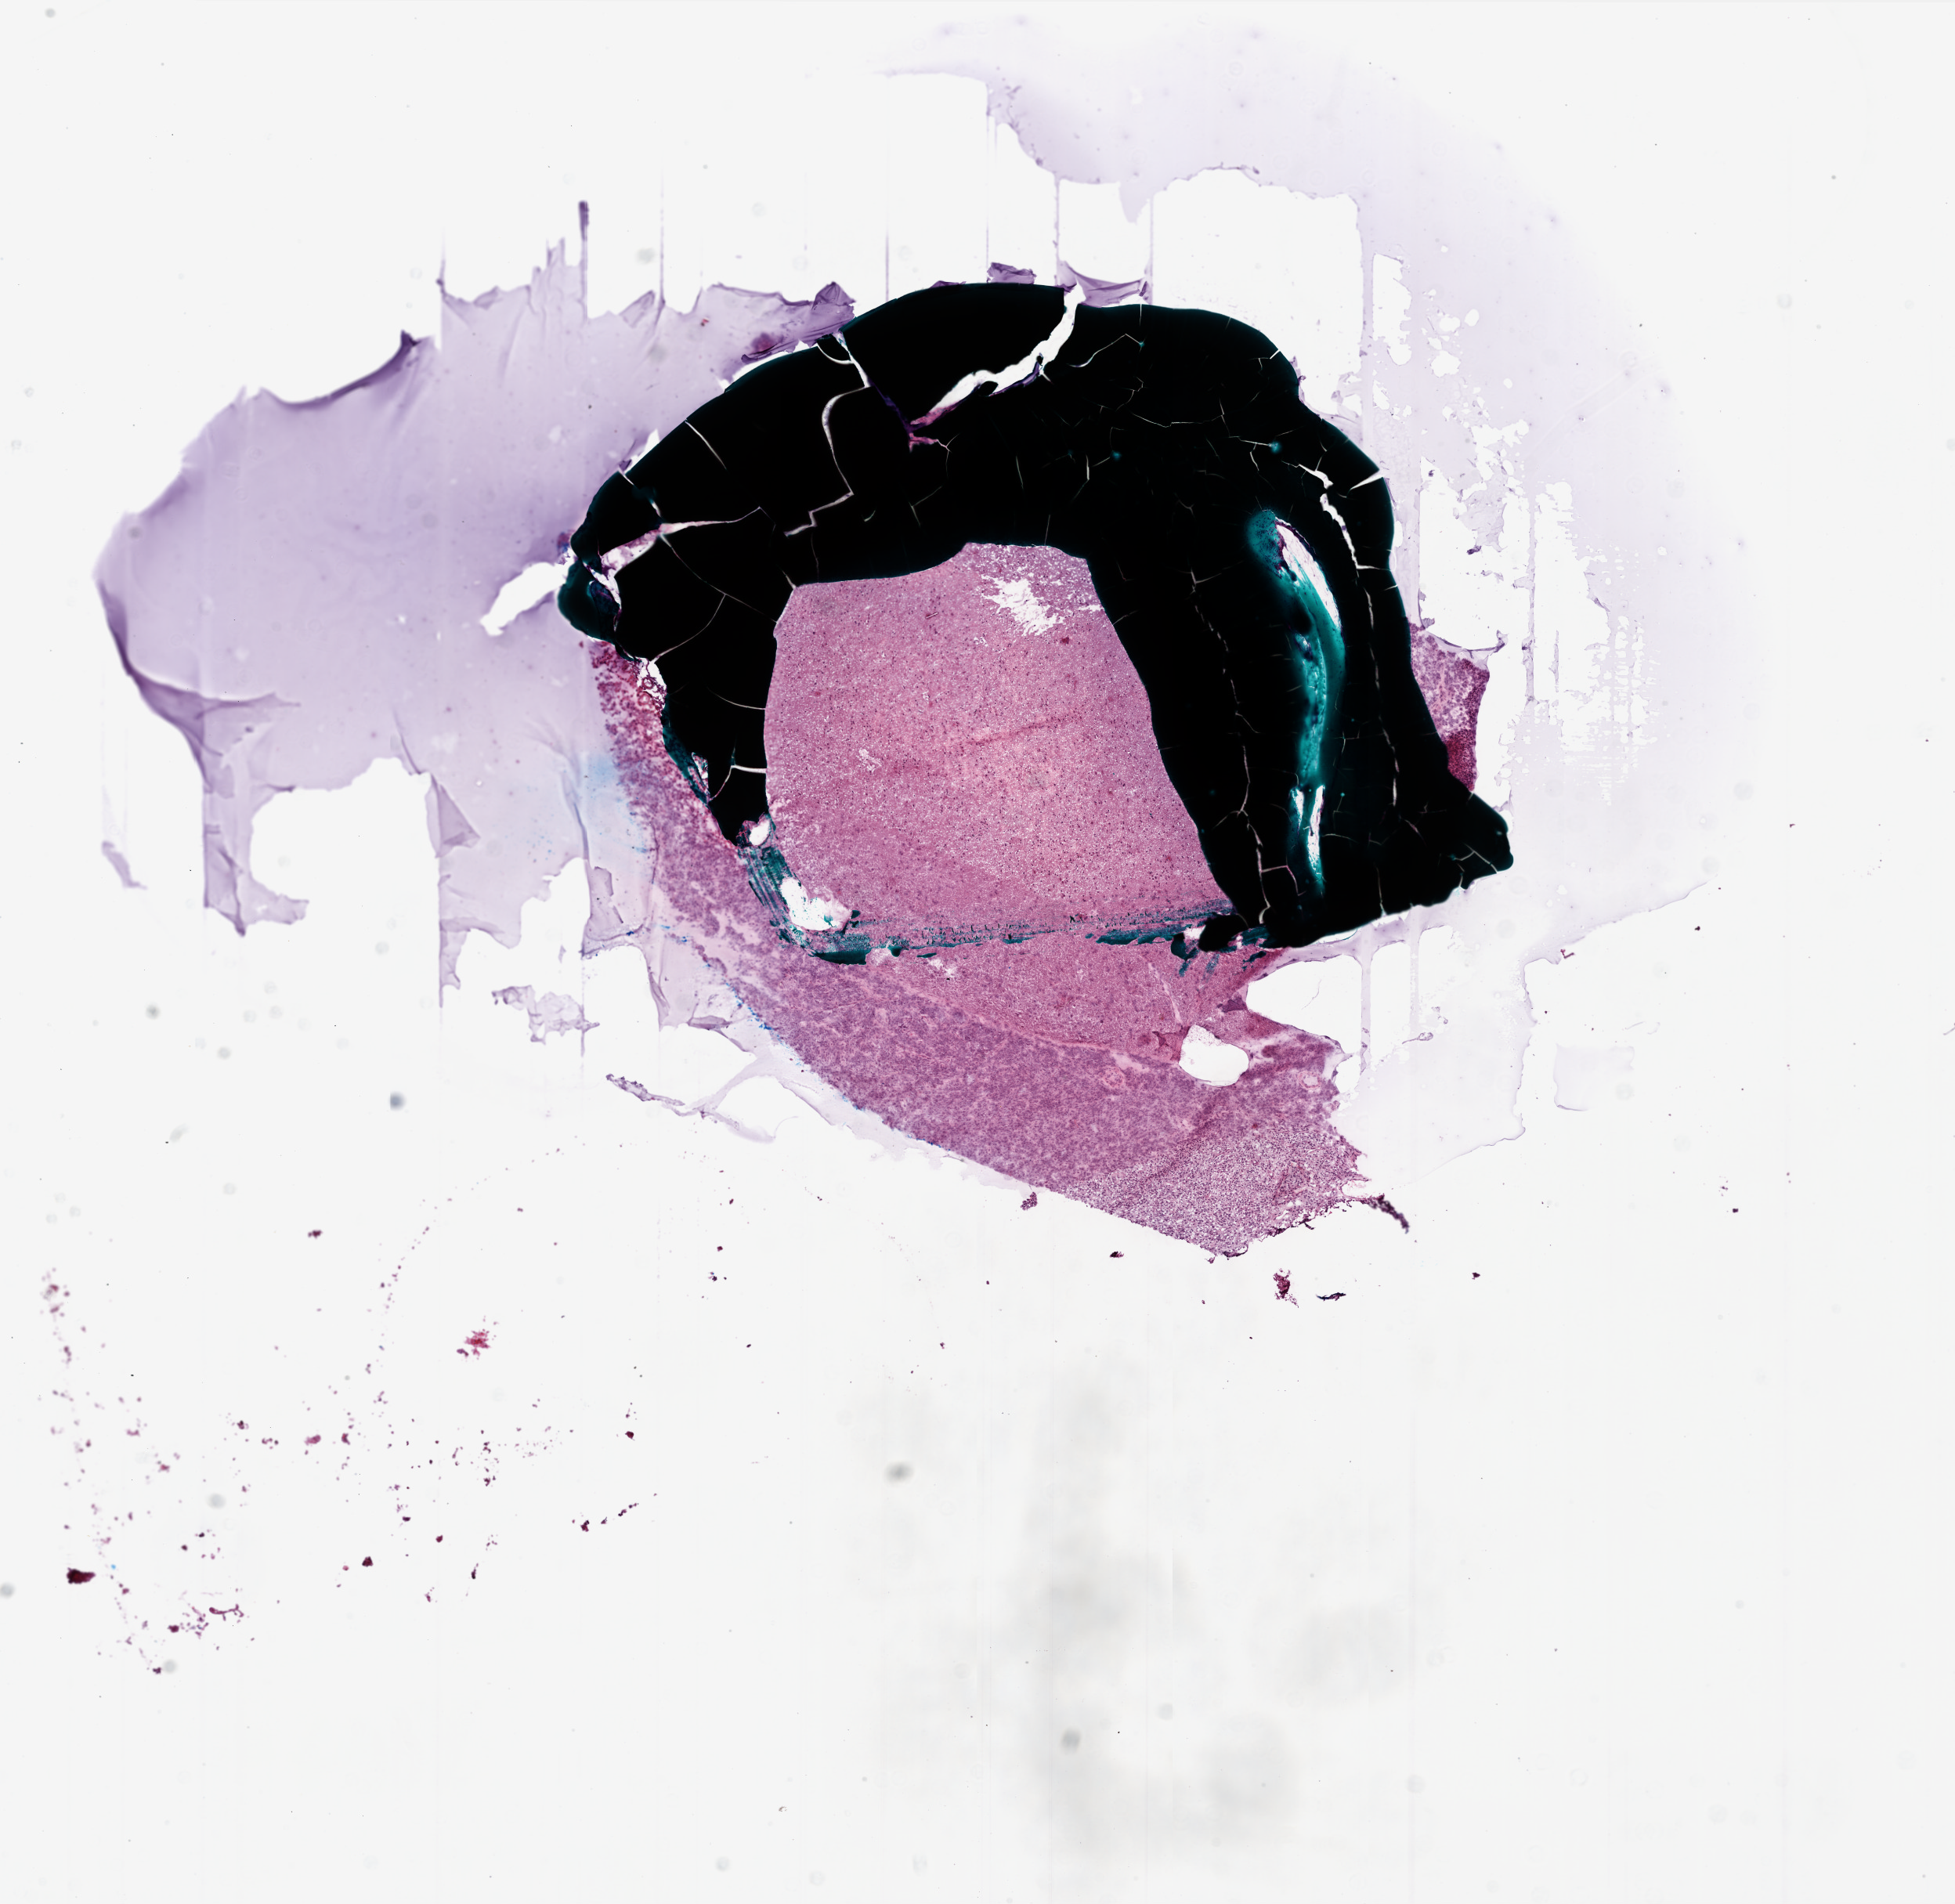
Hematoxylin and eosin (H&E) stained whole-slide image, a low-resolution overview of the entire scanned area, about 10.0 x 9.7 mm (slide scanned at 20x). Frozen section from the bottom of the tissue portion. Sample: primary tumour, brain. Female patient; age at initial diagnosis 63 years. Slide review estimates, as recorded: tumour cells 50%, tumour nuclei 90%, normal cells 0%, stromal cells 50%, necrosis 0%. Inflammatory infiltration, as recorded: lymphocyte infiltration 0%, monocyte infiltration 0%, neutrophil infiltration 0%.
- diagnosis: Glioblastoma